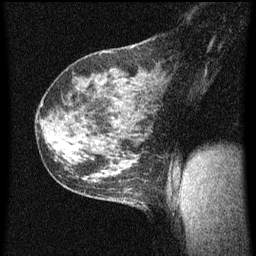
Breast MRI (dynamic contrast-enhanced), one sagittal slice. Position 38 of 60 along the scan axis. Dynamic contrast-enhanced series, image 2 of 3 at this slice position (ordered by acquisition). 1.5 T. TE 4.2 ms, TR 8 ms. 256 × 256 image matrix, field of view 180 × 180 mm. Female patient, age 35 years.
Structures marked on this image (semi-automatic segmentation, software-assisted and operator-edited):
- analysis volume of interest (the breast-tissue region the enhancement analysis was run in; not a lesion): bounding box [x1, y1, x2, y2] px = [106, 182, 149, 211]
- tumour enhancement mask (voxels above the 70 % enhancement threshold inside the analysis volume of interest): [124, 188, 133, 201]